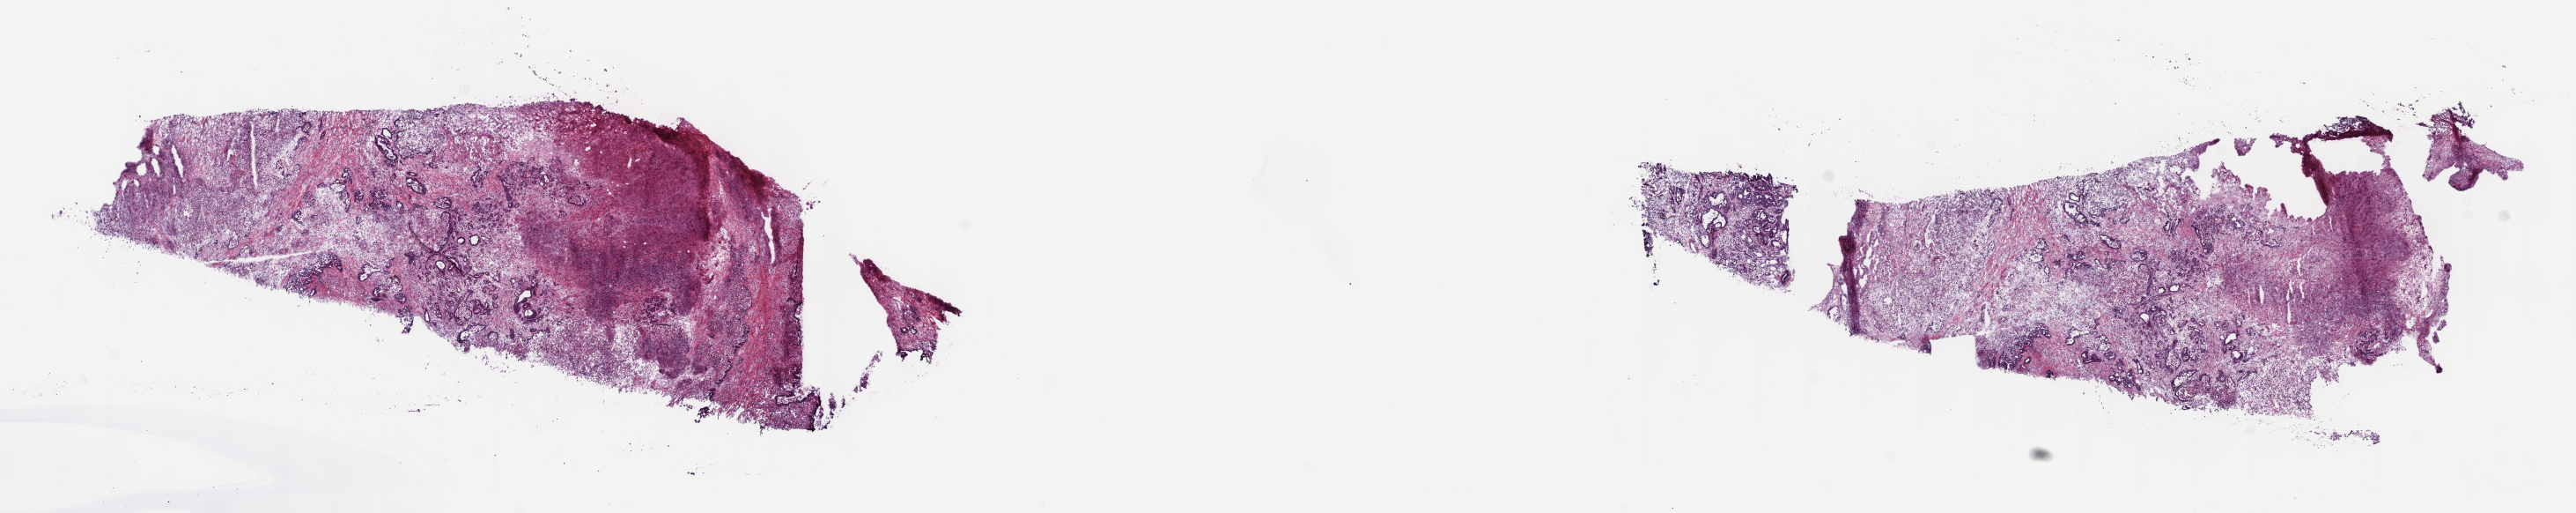
Whole-slide histology image, H&E-stained, shown as a low-resolution overview of the whole scanned area (about 23.7 x 4.7 mm, acquisition: 40x scan). Frozen section from the top of the tissue portion. Primary tumour sample from the pancreas. Patient: male, age at initial diagnosis 47 years.
Diagnosis: Infiltrating duct carcinoma, NOS (head of pancreas).